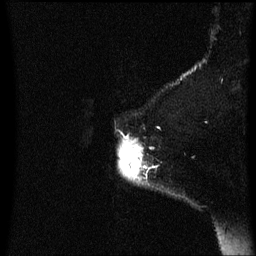
Breast MRI (dynamic contrast-enhanced), one sagittal slice. Dynamic contrast-enhanced series, image 2 of 3 at this slice position (ordered by acquisition). 1.5 T. TE 4.2 ms, TR 8.4 ms. 256 × 256 image matrix. Female patient, age 54 years. From the clinical record (not read from this slice): setting: breast cancer imaged before/during neoadjuvant chemotherapy; receptor status: HR-positive, HER2-negative.
Outlined on this slice (semi-automatic segmentation, software-assisted and operator-edited):
- analysis volume of interest (the breast-tissue region the enhancement analysis was run in; not a lesion): bounding box [x1, y1, x2, y2] px = [120, 138, 153, 187]
- tumour enhancement mask (voxels above the 70 % enhancement threshold inside the analysis volume of interest): [120, 138, 153, 179]